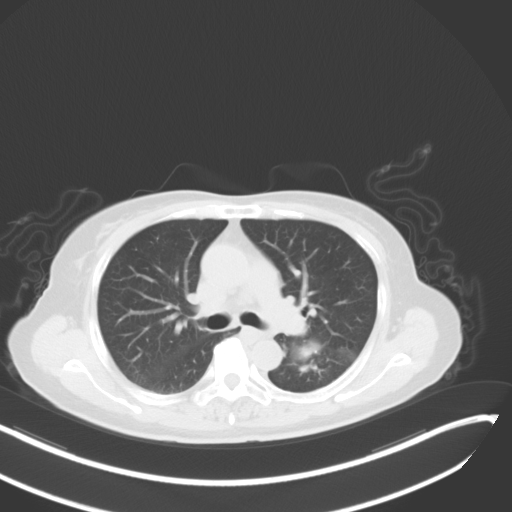
Chest CT, one axial slice; position 25 of 48 along the scan axis; reconstruction kernel B31f; 120 kVp; lung window (W 1500 / L -600 HU); 5 mm slice thickness; 512 × 512 image matrix. Female patient, age 64 years. From the clinical record (not read from this slice): clinical TNM (as recorded): T3 N1 M1.
Outlined on this slice (rectangle marked by the reading radiologist):
- lung tumour (recorded histology: small cell carcinoma): box from (x=283, y=329) to (x=328, y=379) px